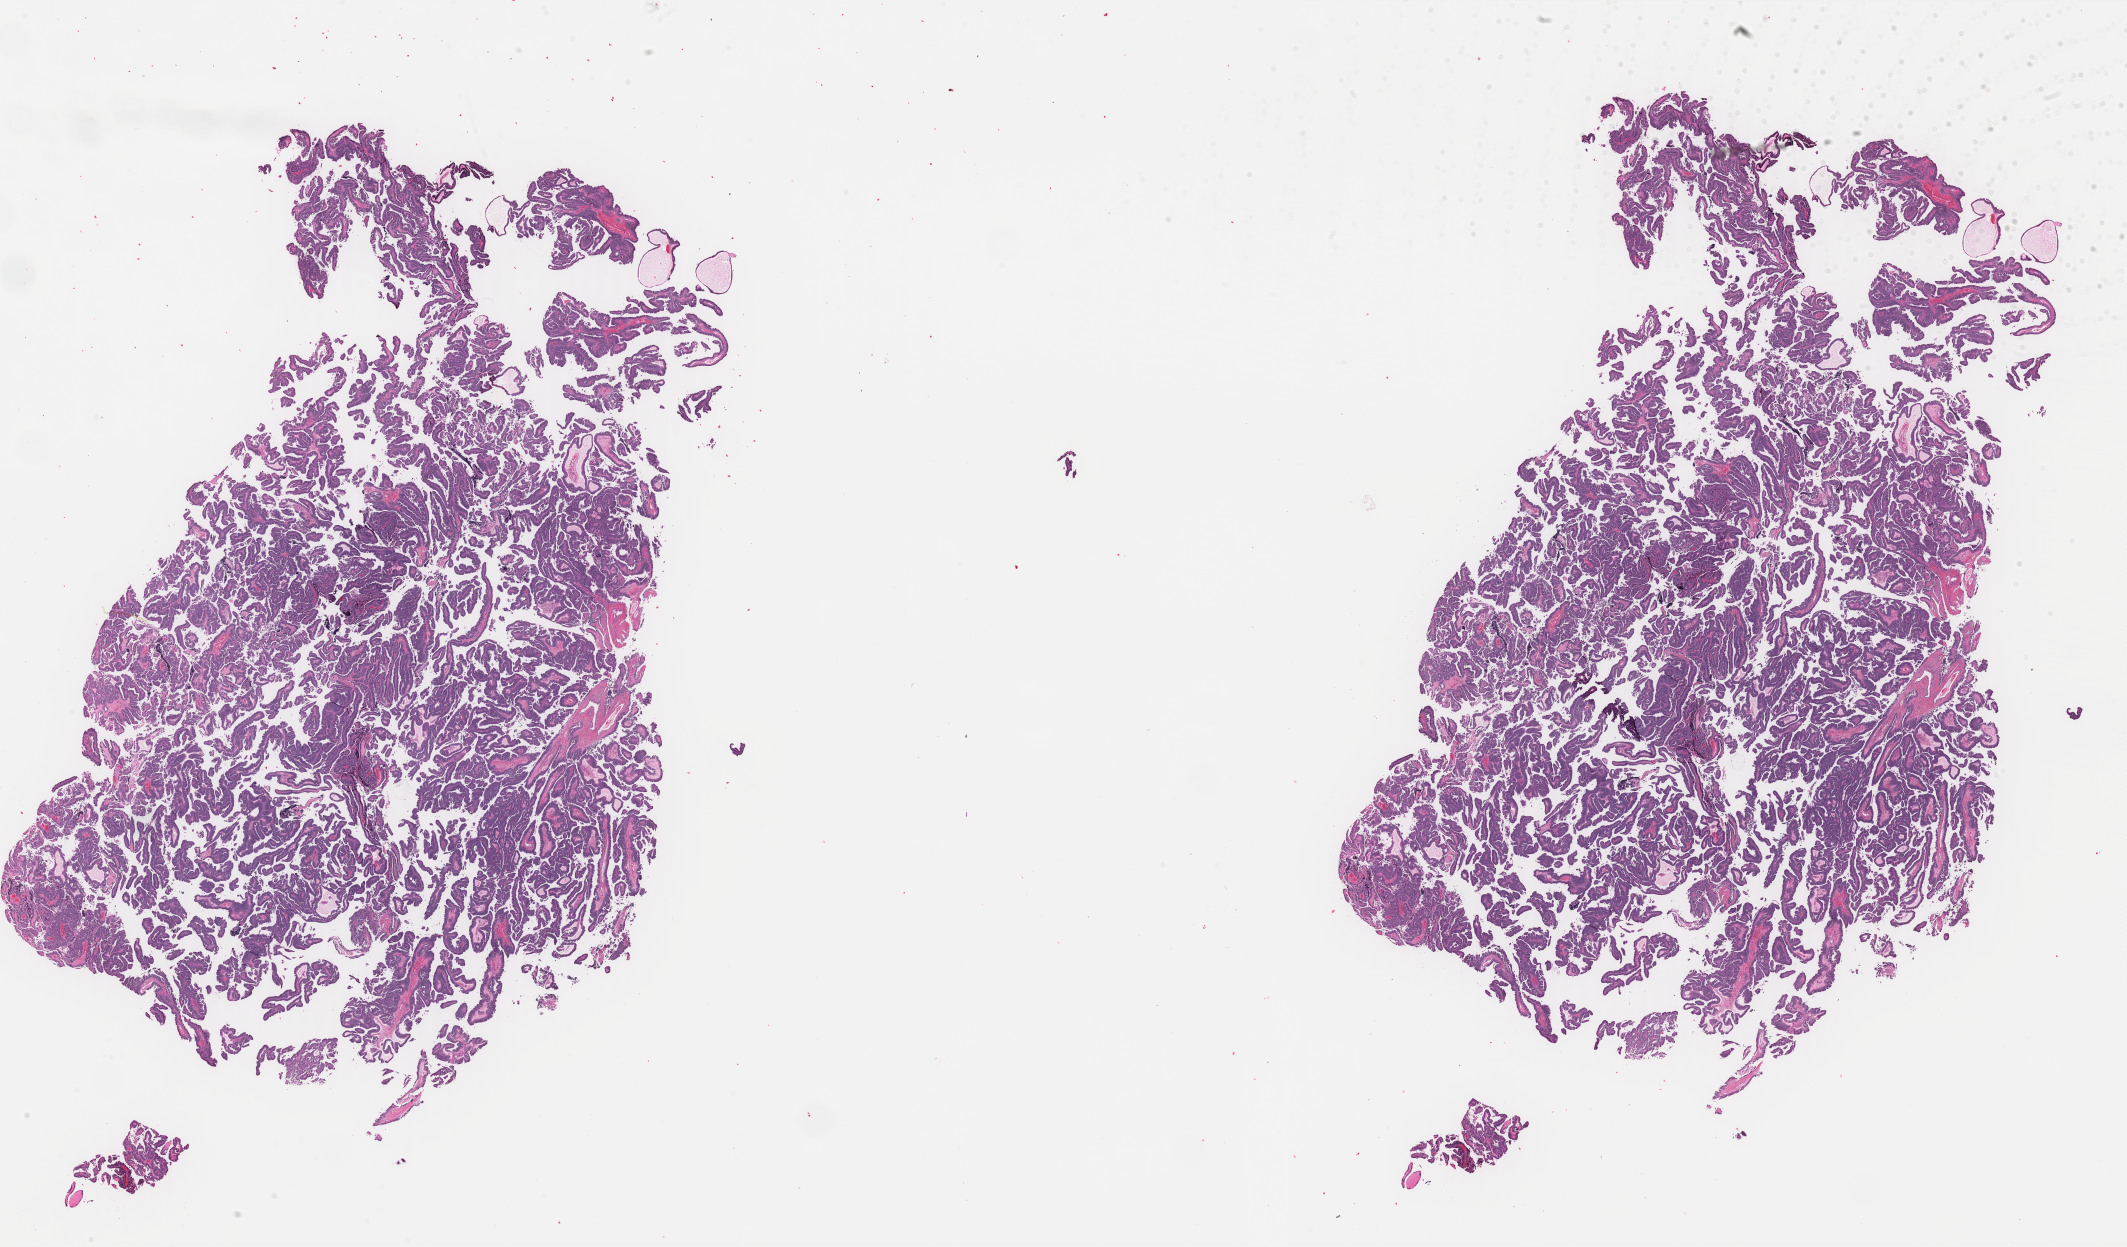
Whole-slide histology image, H&E-stained — shown as a low-resolution overview of the whole scanned area (about 33.7 x 19.7 mm); FFPE section; ovary, primary tumour sample. Female patient; age at initial diagnosis 48 years. Histologic grade: G3 (poorly differentiated).
- FIGO stage: IIIB
- diagnosis: Papillary serous cystadenocarcinoma
- laterality: right